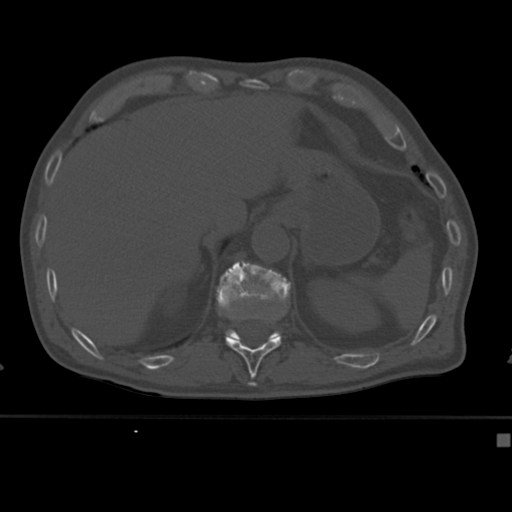
CT including the spine, one axial slice; slice 203 of 430 in the series (ordered by position); reconstruction kernel Br40s; 120 kVp; bone window (W 1800 / L 400 HU); 512 × 512 image matrix, field of view 337 × 337 mm. Male patient, age 64 years. From the clinical record (not read from this slice): primary cancer: uterus; vertebrae with lytic lesions (as recorded): T1, T4, T5, T7, L5.
Annotated regions visible in this slice (semi-automatic segmentation, software-assisted and operator-edited):
- T11 vertebra: box from (x=225, y=311) to (x=286, y=379) px
- T12 vertebra: (x=216, y=261)–(x=291, y=339)